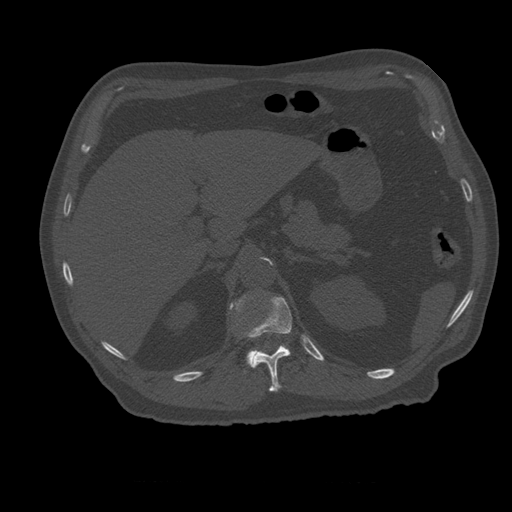
CT including the spine, one axial slice; slice 256 of 399 in the series (ordered by position); reconstruction kernel STANDARD; 120 kVp; bone window (W 1800 / L 400 HU); 512 × 512 image matrix. Patient age 73 years. Case-level facts recorded for this patient, not image findings: primary cancer: prostate; vertebrae with lytic lesions (as recorded): L2.
Structures marked on this image (semi-automatically segmented with operator editing):
- L1 vertebra: bounding box [x1, y1, x2, y2] px = [230, 296, 291, 367]
- T12 vertebra: [248, 297, 292, 392]